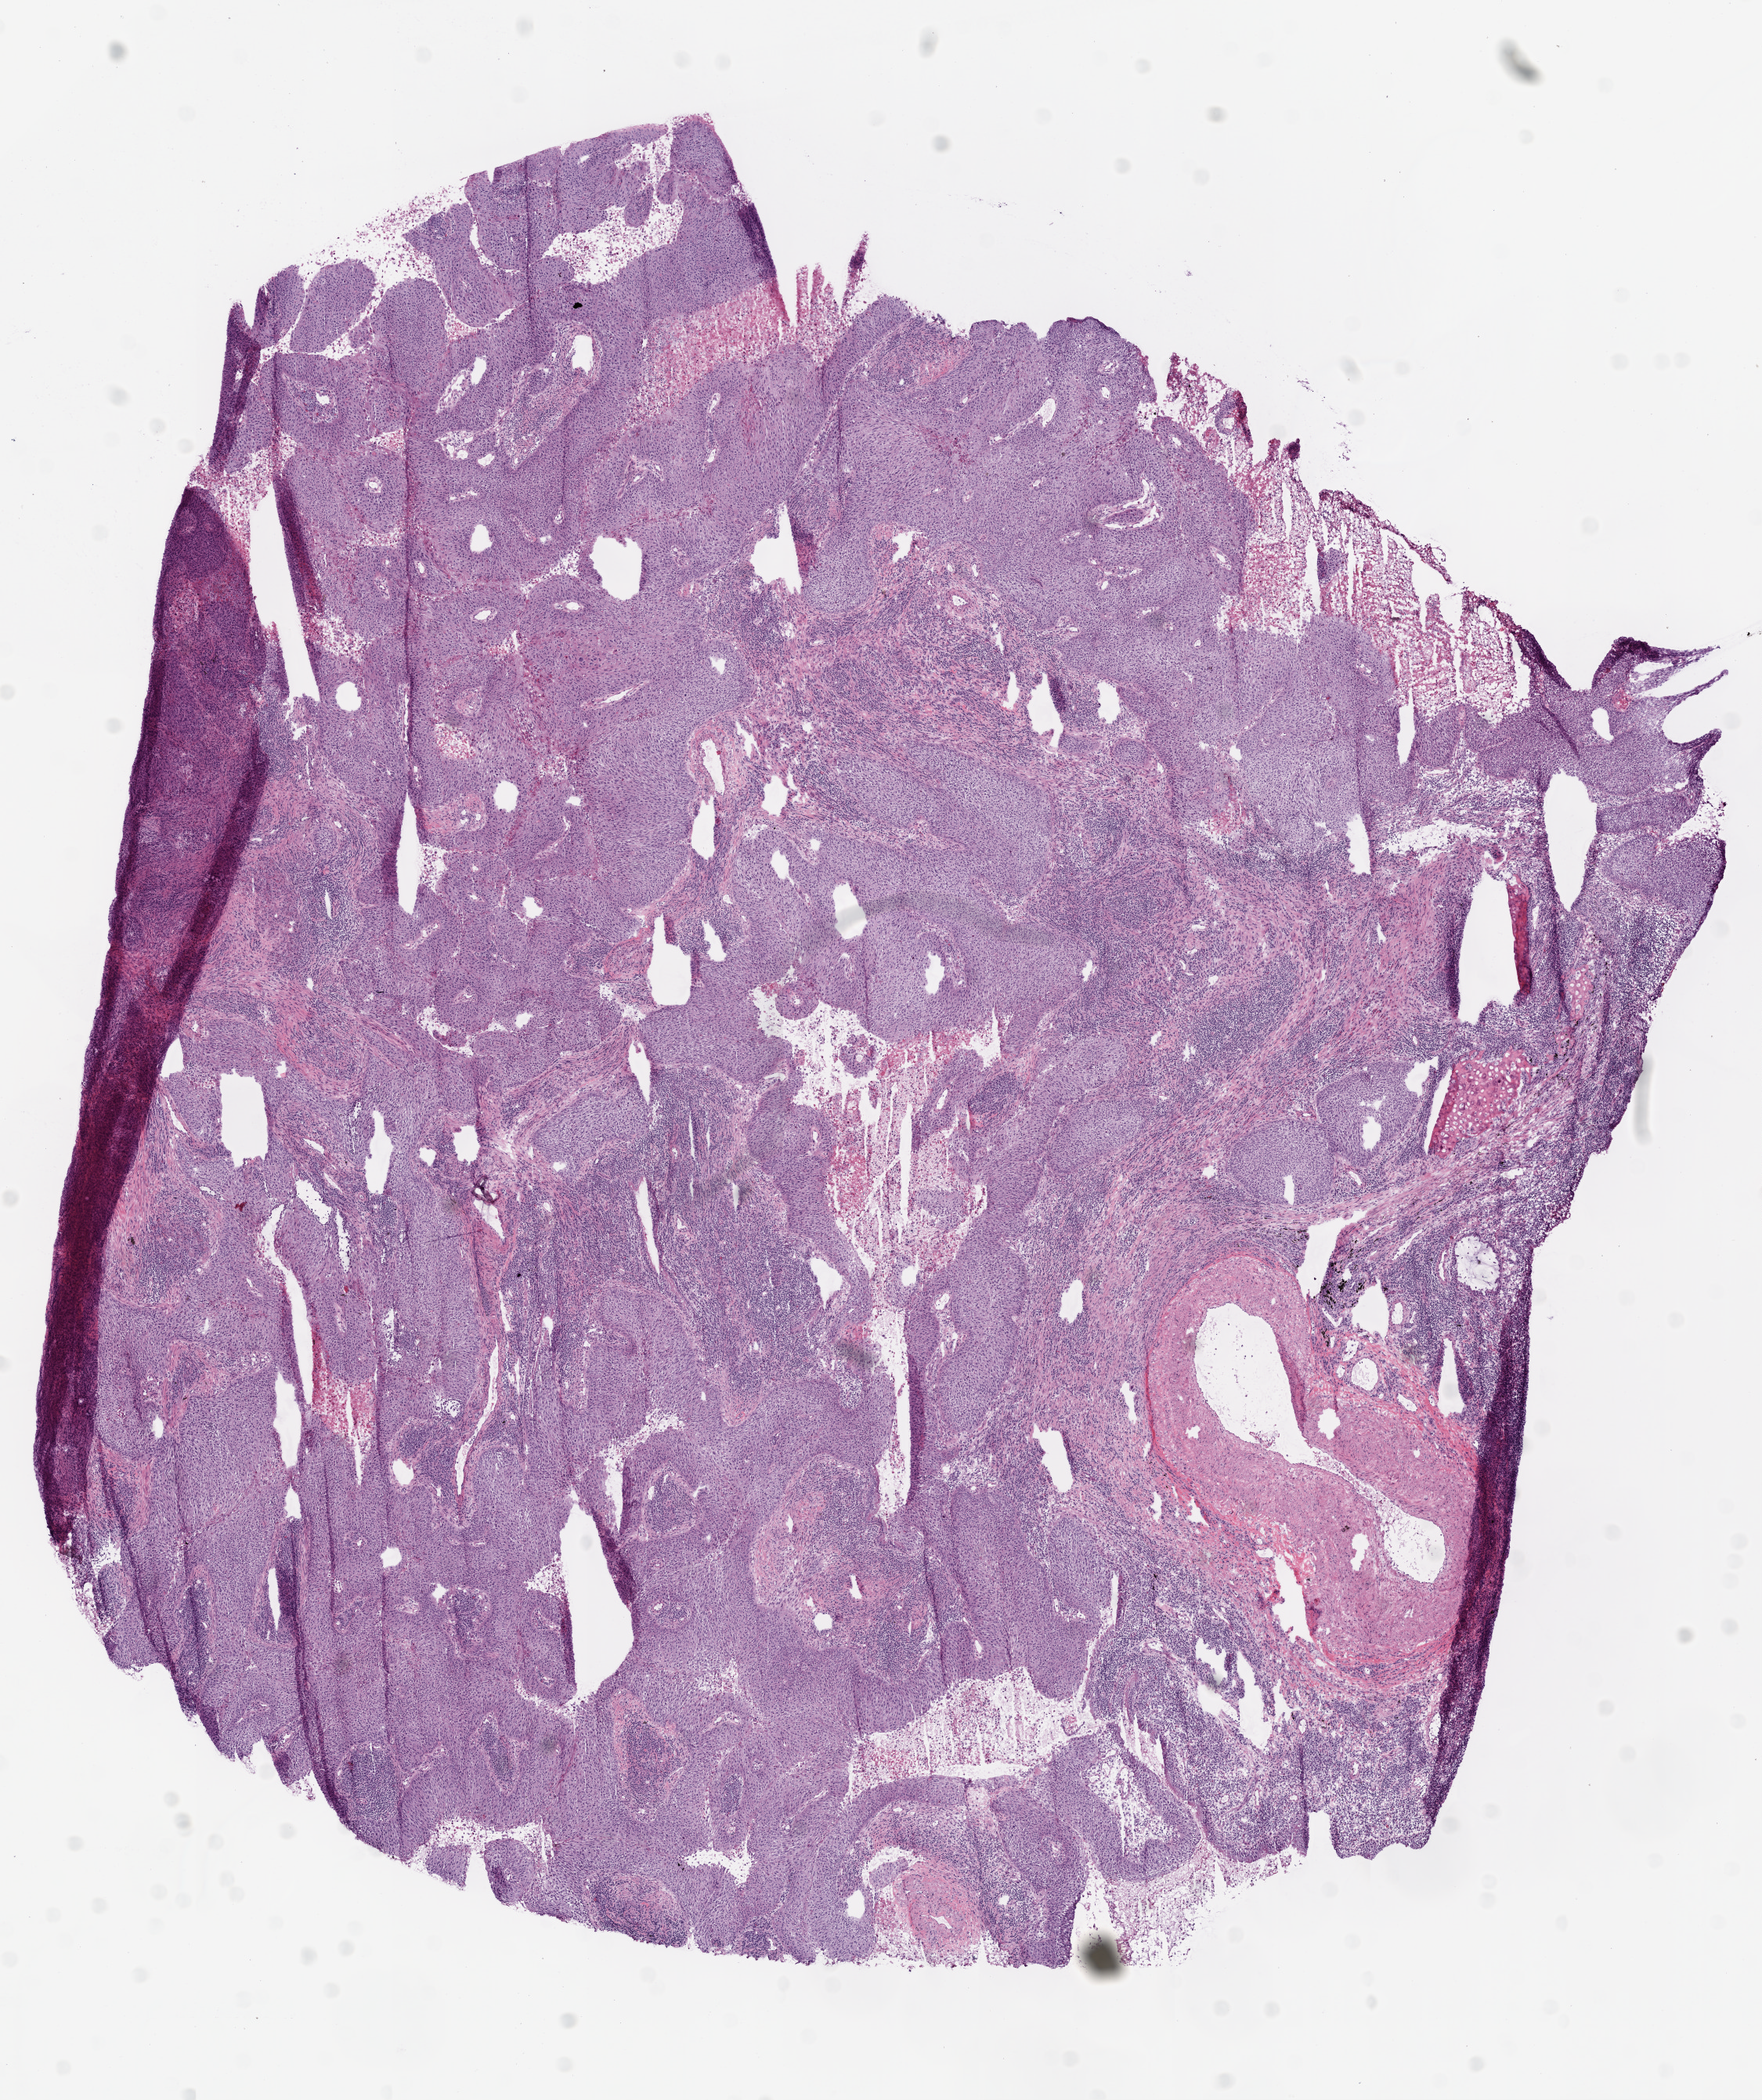
Whole-slide histology image, Hematoxylin and eosin (H&E) stained — shown as a low-resolution overview of the whole scanned area (about 9.0 x 10.8 mm, slide scanned at 20x), frozen section from the bottom of the tissue portion, primary tumour sample from the lung. Male, age 67 years at initial diagnosis. Slide review estimates, as recorded: tumour cells 77%, tumour nuclei 65%, normal cells 3%, stromal cells 10%, necrosis 10%. Infiltration values recorded for this section: lymphocyte infiltration 25%, monocyte infiltration 0%, neutrophil infiltration 0%.
TNM: T2 N3 M0. Diagnosis: Squamous cell carcinoma, NOS. AJCC pathologic stage: IIIB (6th edition). Laterality: left.